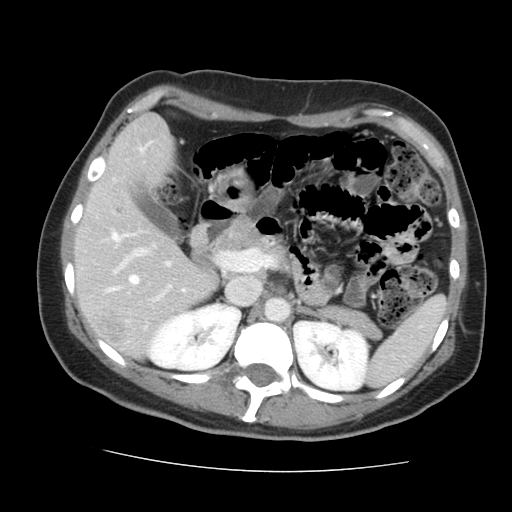
Contrast-enhanced abdominal CT, one axial slice. Position 86 of 144 along the scan axis. 120 kVp. Intravenous contrast given. Soft-tissue window (W 400 / L 40 HU). 2.5 mm slice thickness. 512 × 512 image matrix. Female patient, age 46 years. From the clinical record (not read from this slice): diagnosis: colorectal cancer liver metastases, imaged before liver resection; multiple liver metastases: no; largest metastasis: 2.8 cm; disease in both lobes: no.
Annotated regions visible in this slice (outlined manually by an expert reader):
- hepatic veins: bounding box <111,149,142,290> (left, top, right, bottom; pixels)
- liver: <77,116,213,354>
- planned liver remnant (the part of the liver to remain after resection): <77,116,213,349>
- portal vein (with intrahepatic branches): <112,233,226,301>
- liver metastasis: <97,317,124,340>